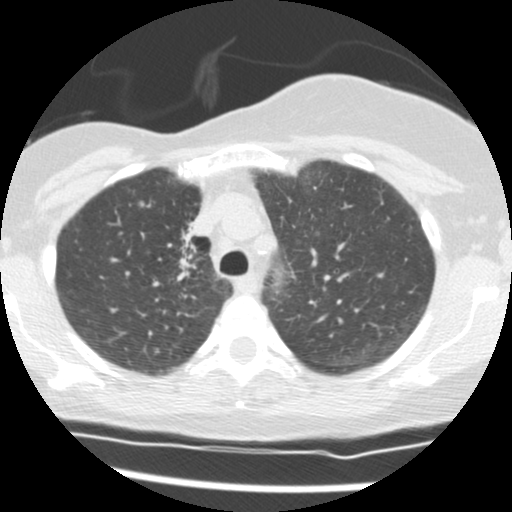
Low-dose screening chest CT, axial slice. Second annual screen. Lung window (W 1500 / L -600 HU). 2.5 mm slice thickness. Standard (soft-tissue) reconstruction kernel (STANDARD). 512 × 512 image matrix, field of view 296 × 296 mm. Female participant, aged 56 years at enrolment. Current smoker at enrolment.
Expert-annotated lung lesion, bounding box <155,215,216,285> (left, top, right, bottom; pixels). The screening reader recorded 2 non-calcified nodules or masses ≥4 mm on this exam; which of them this box marks is not recorded. Official screen result: positive, change unspecified: nodule(s) >= 4 mm or enlarging nodule(s), mass(es), or other non-specific abnormalities suspicious for lung cancer. Lung cancer was diagnosed 675 days after this screen: adenocarcinoma, NOS, right upper lobe, stage IIIB (AJCC 6th edition), 8 mm at pathology.